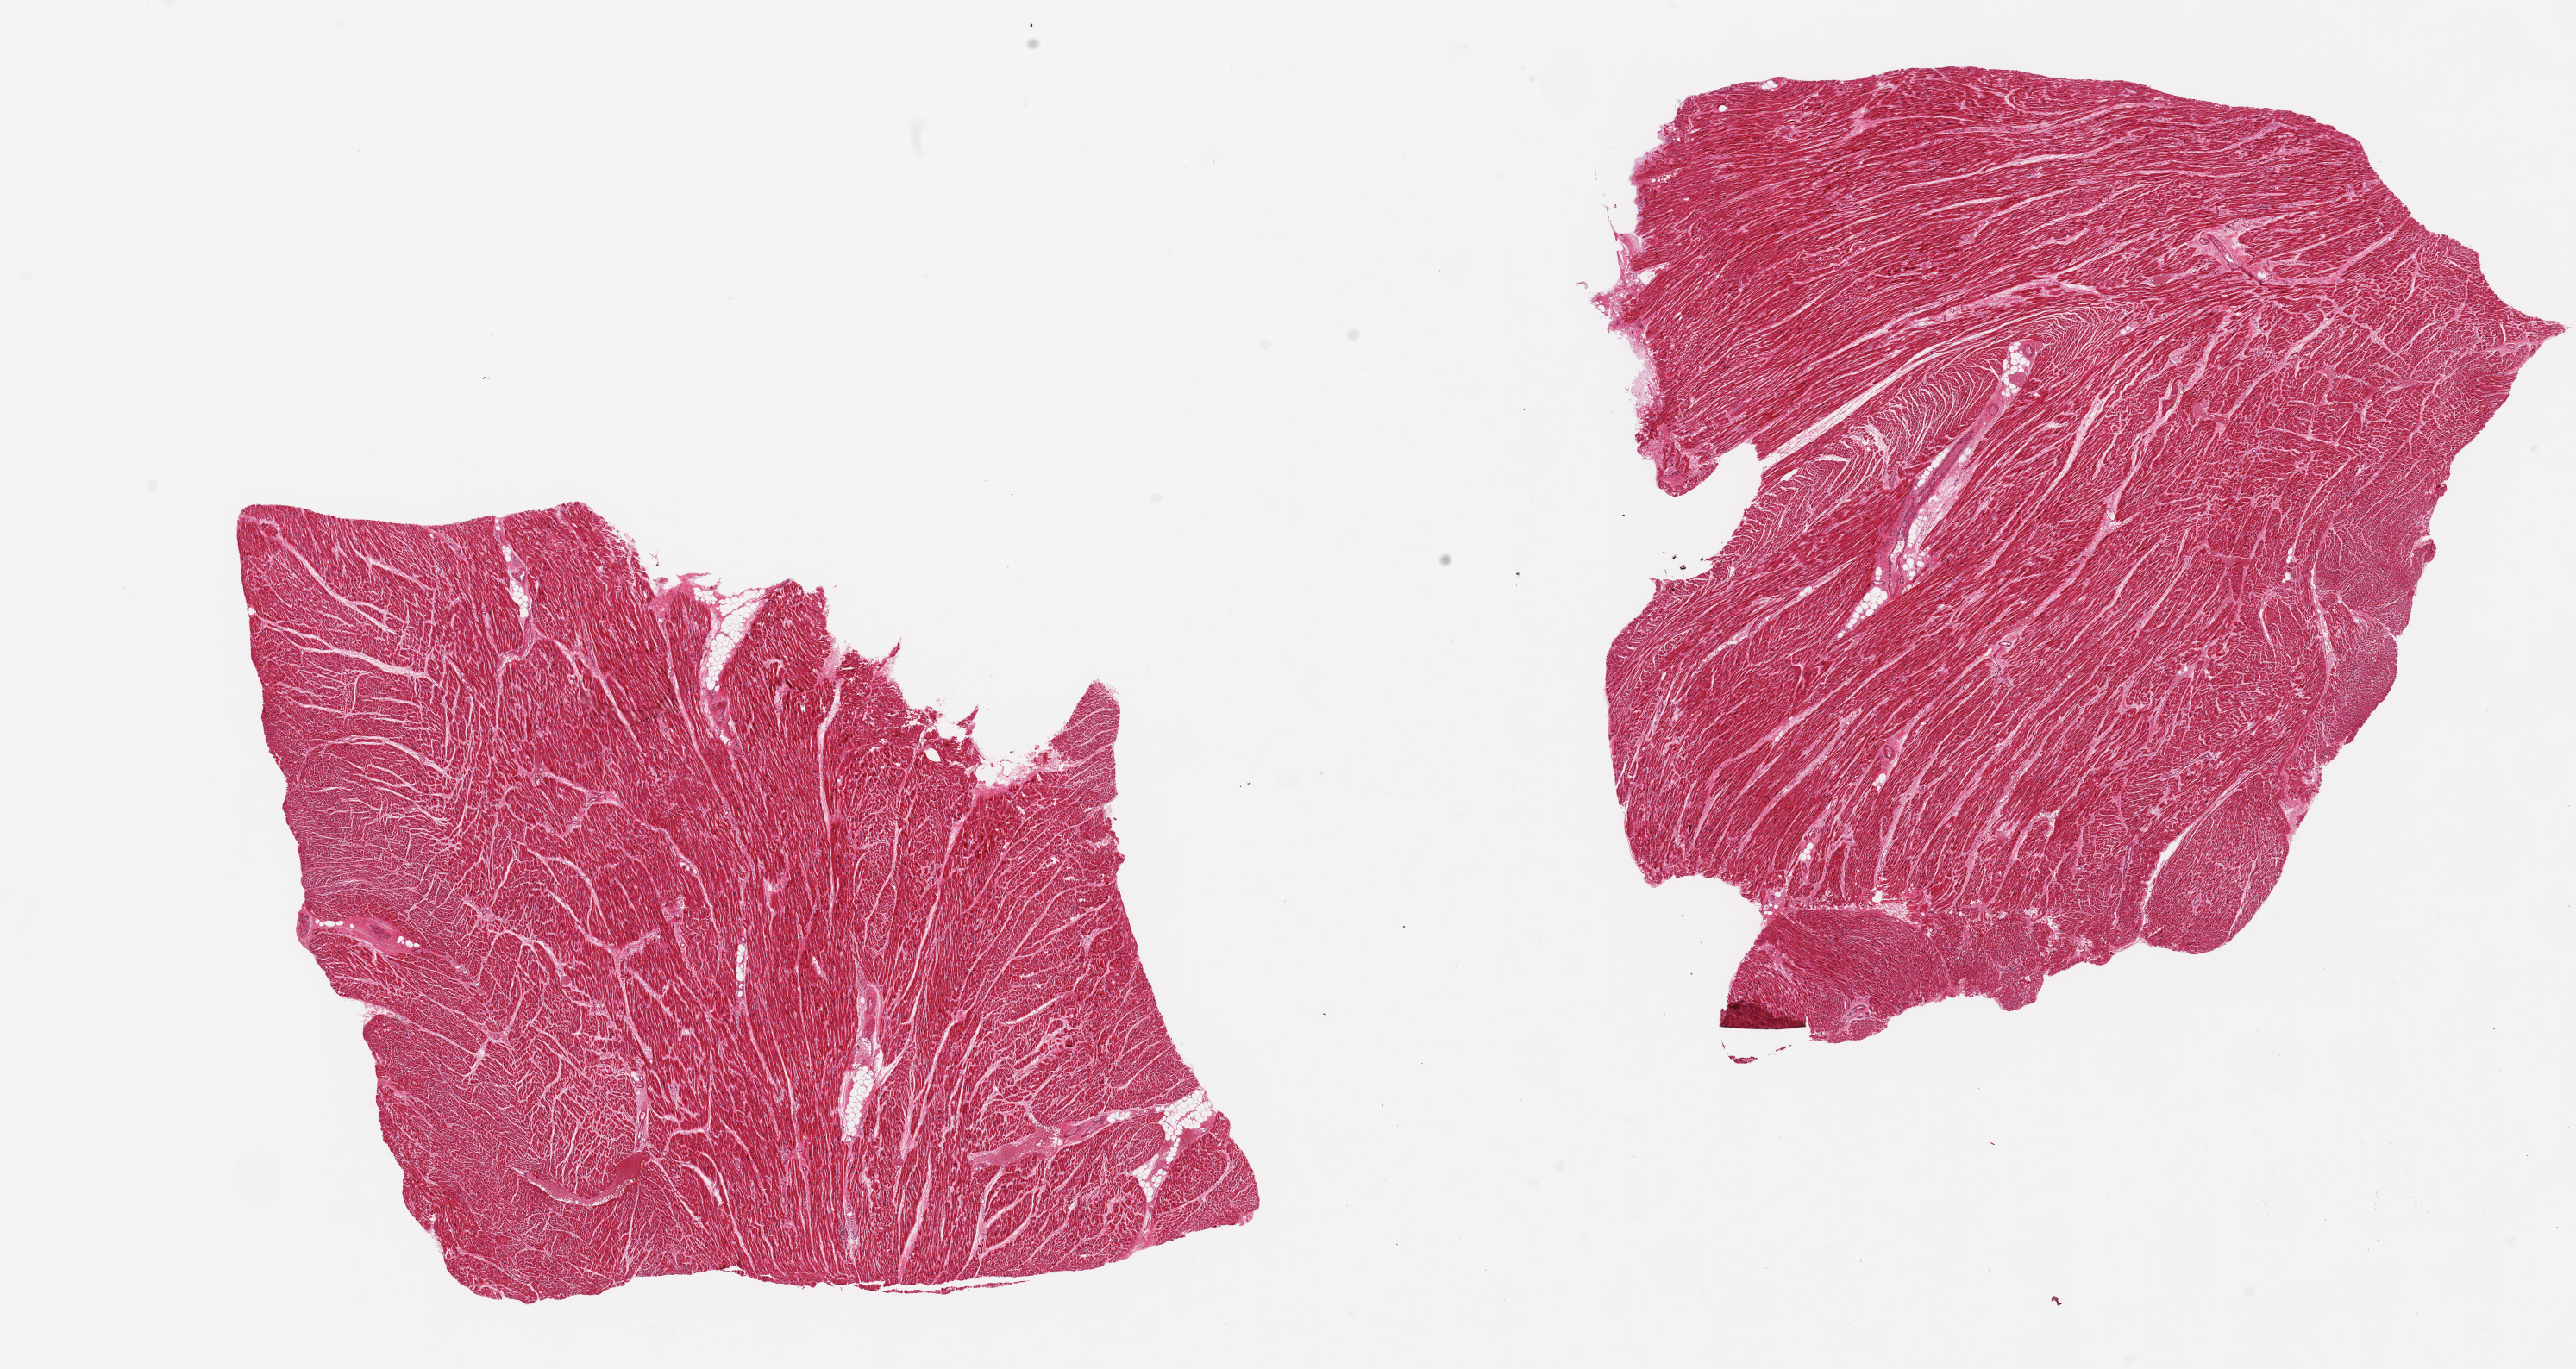
Haematoxylin and eosin whole-slide image, whole scanned area (about 23.6 x 12.6 mm) shown as a low-resolution overview. PAXgene-fixed paraffin-embedded (PFPE) section. Target tissue: heart. Donor tissue sample. Male donor.
* review note (as recorded): 2 pieces, 8x8 & 10x9mm